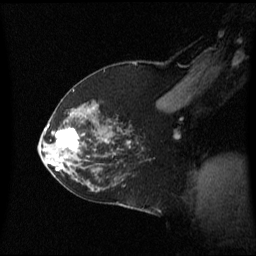
Breast MRI (dynamic contrast-enhanced), one sagittal slice; position 40 of 60 along the scan axis; dynamic contrast-enhanced series, image 2 of 3 at this slice position (ordered by acquisition); 1.5 T; TE 4.2 ms, TR 8.4 ms; 2 mm slice thickness; 256 × 256 image matrix, field of view 240 × 240 mm. Female patient, age 59 years. Case-level facts recorded for this patient, not image findings: setting: breast cancer imaged before/during neoadjuvant chemotherapy; receptor status: HR-positive, HER2-negative.
Outlined on this slice (semi-automatic segmentation, software-assisted and operator-edited):
- analysis volume of interest (the breast-tissue region the enhancement analysis was run in; not a lesion): bounding box <46,114,89,163> (left, top, right, bottom; pixels)
- tumour enhancement mask (voxels above the 70 % enhancement threshold inside the analysis volume of interest): <55,128,78,153>